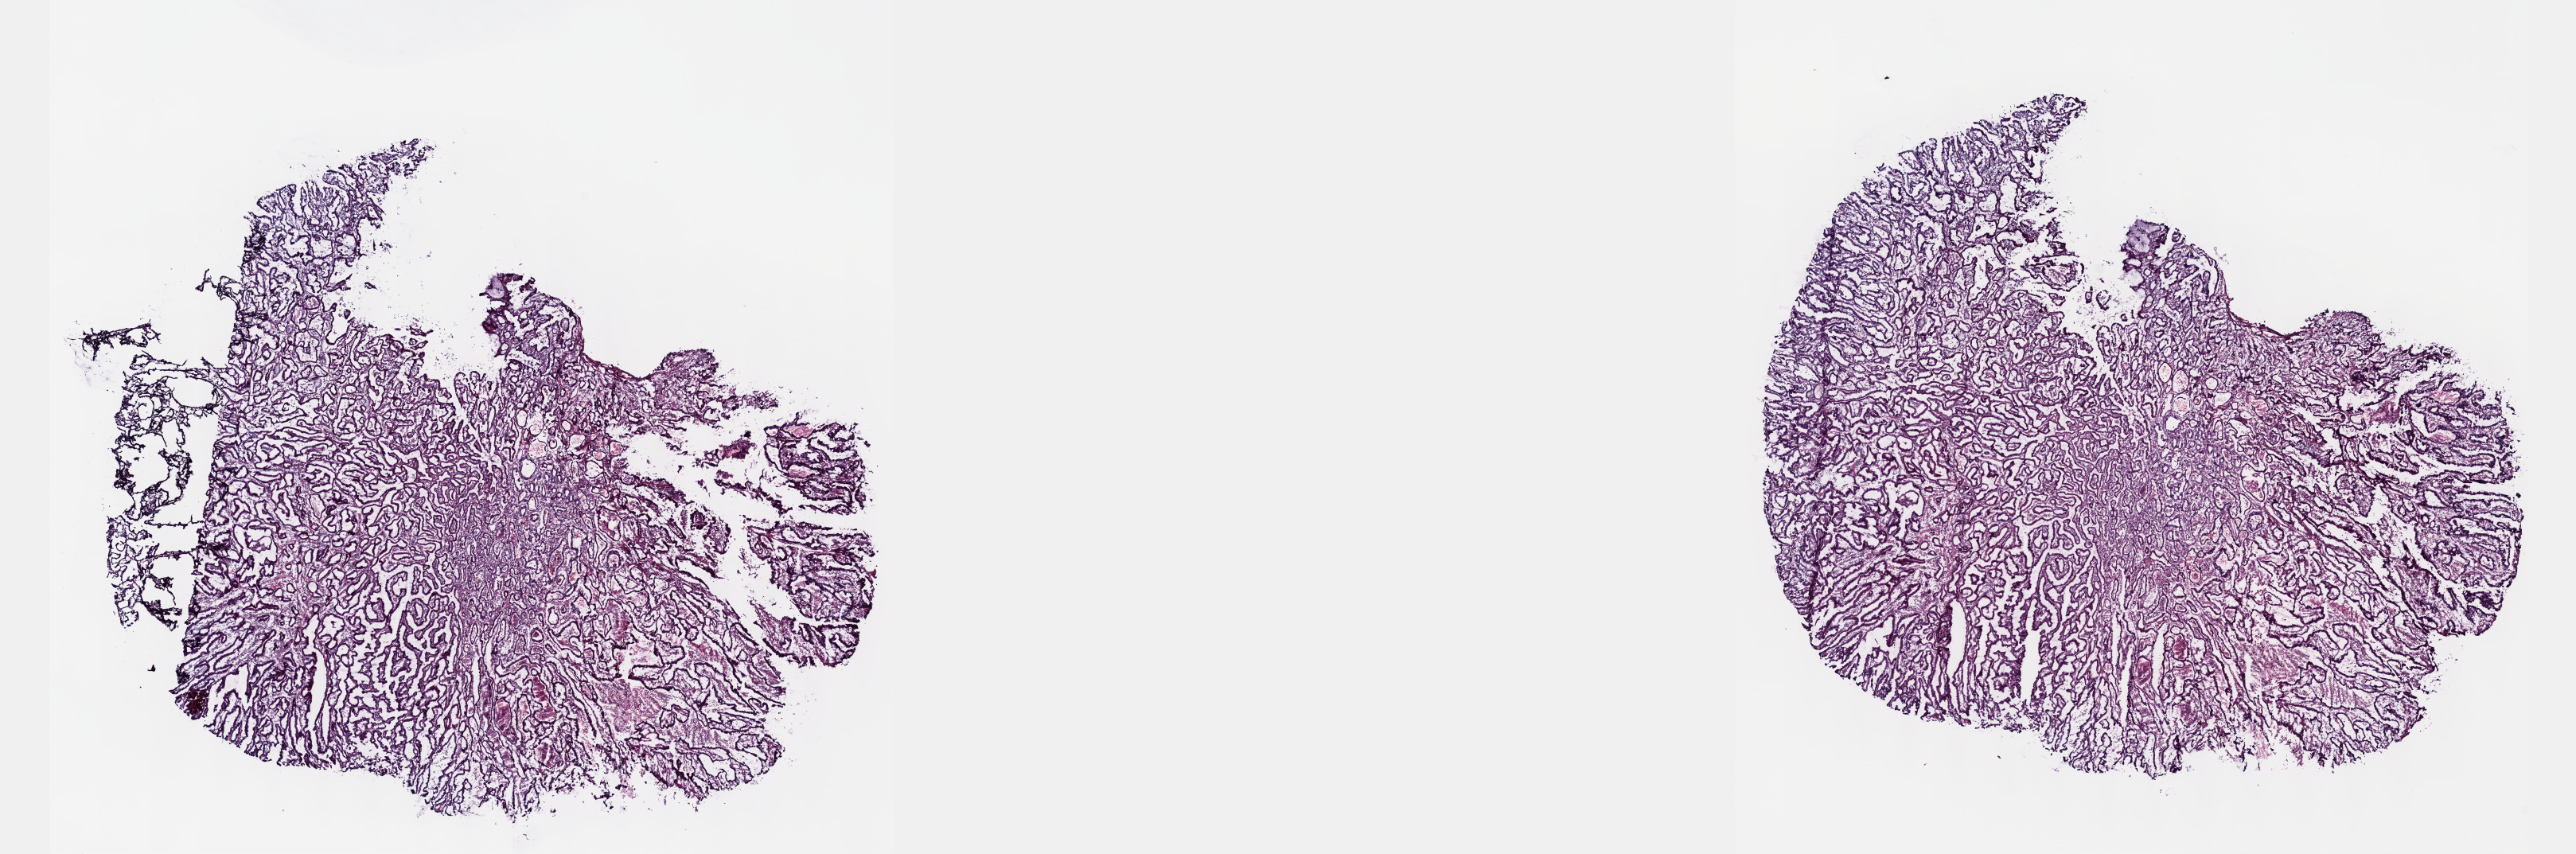
Hematoxylin and eosin (H&E) stained whole-slide image — a low-resolution overview of the entire scanned area, about 26.2 x 8.7 mm. Frozen section. Stomach, primary tumour sample. Male patient; age at initial diagnosis 68 years. Histologic grade: G3 (poorly differentiated). Composition of this section per pathologist review: tumour cells 83%, tumour nuclei 65%, normal cells 0%, stromal cells 0%, necrosis 17%. Infiltration values recorded for this section: lymphocyte infiltration 5%, monocyte infiltration 0%, neutrophil infiltration 0%.
- diagnosis: Adenocarcinoma, intestinal type
- lymph nodes positive (case pathology): 6 of 23 examined
- TNM: T3 N2 M0
- AJCC pathologic stage: IIIA (7th edition)